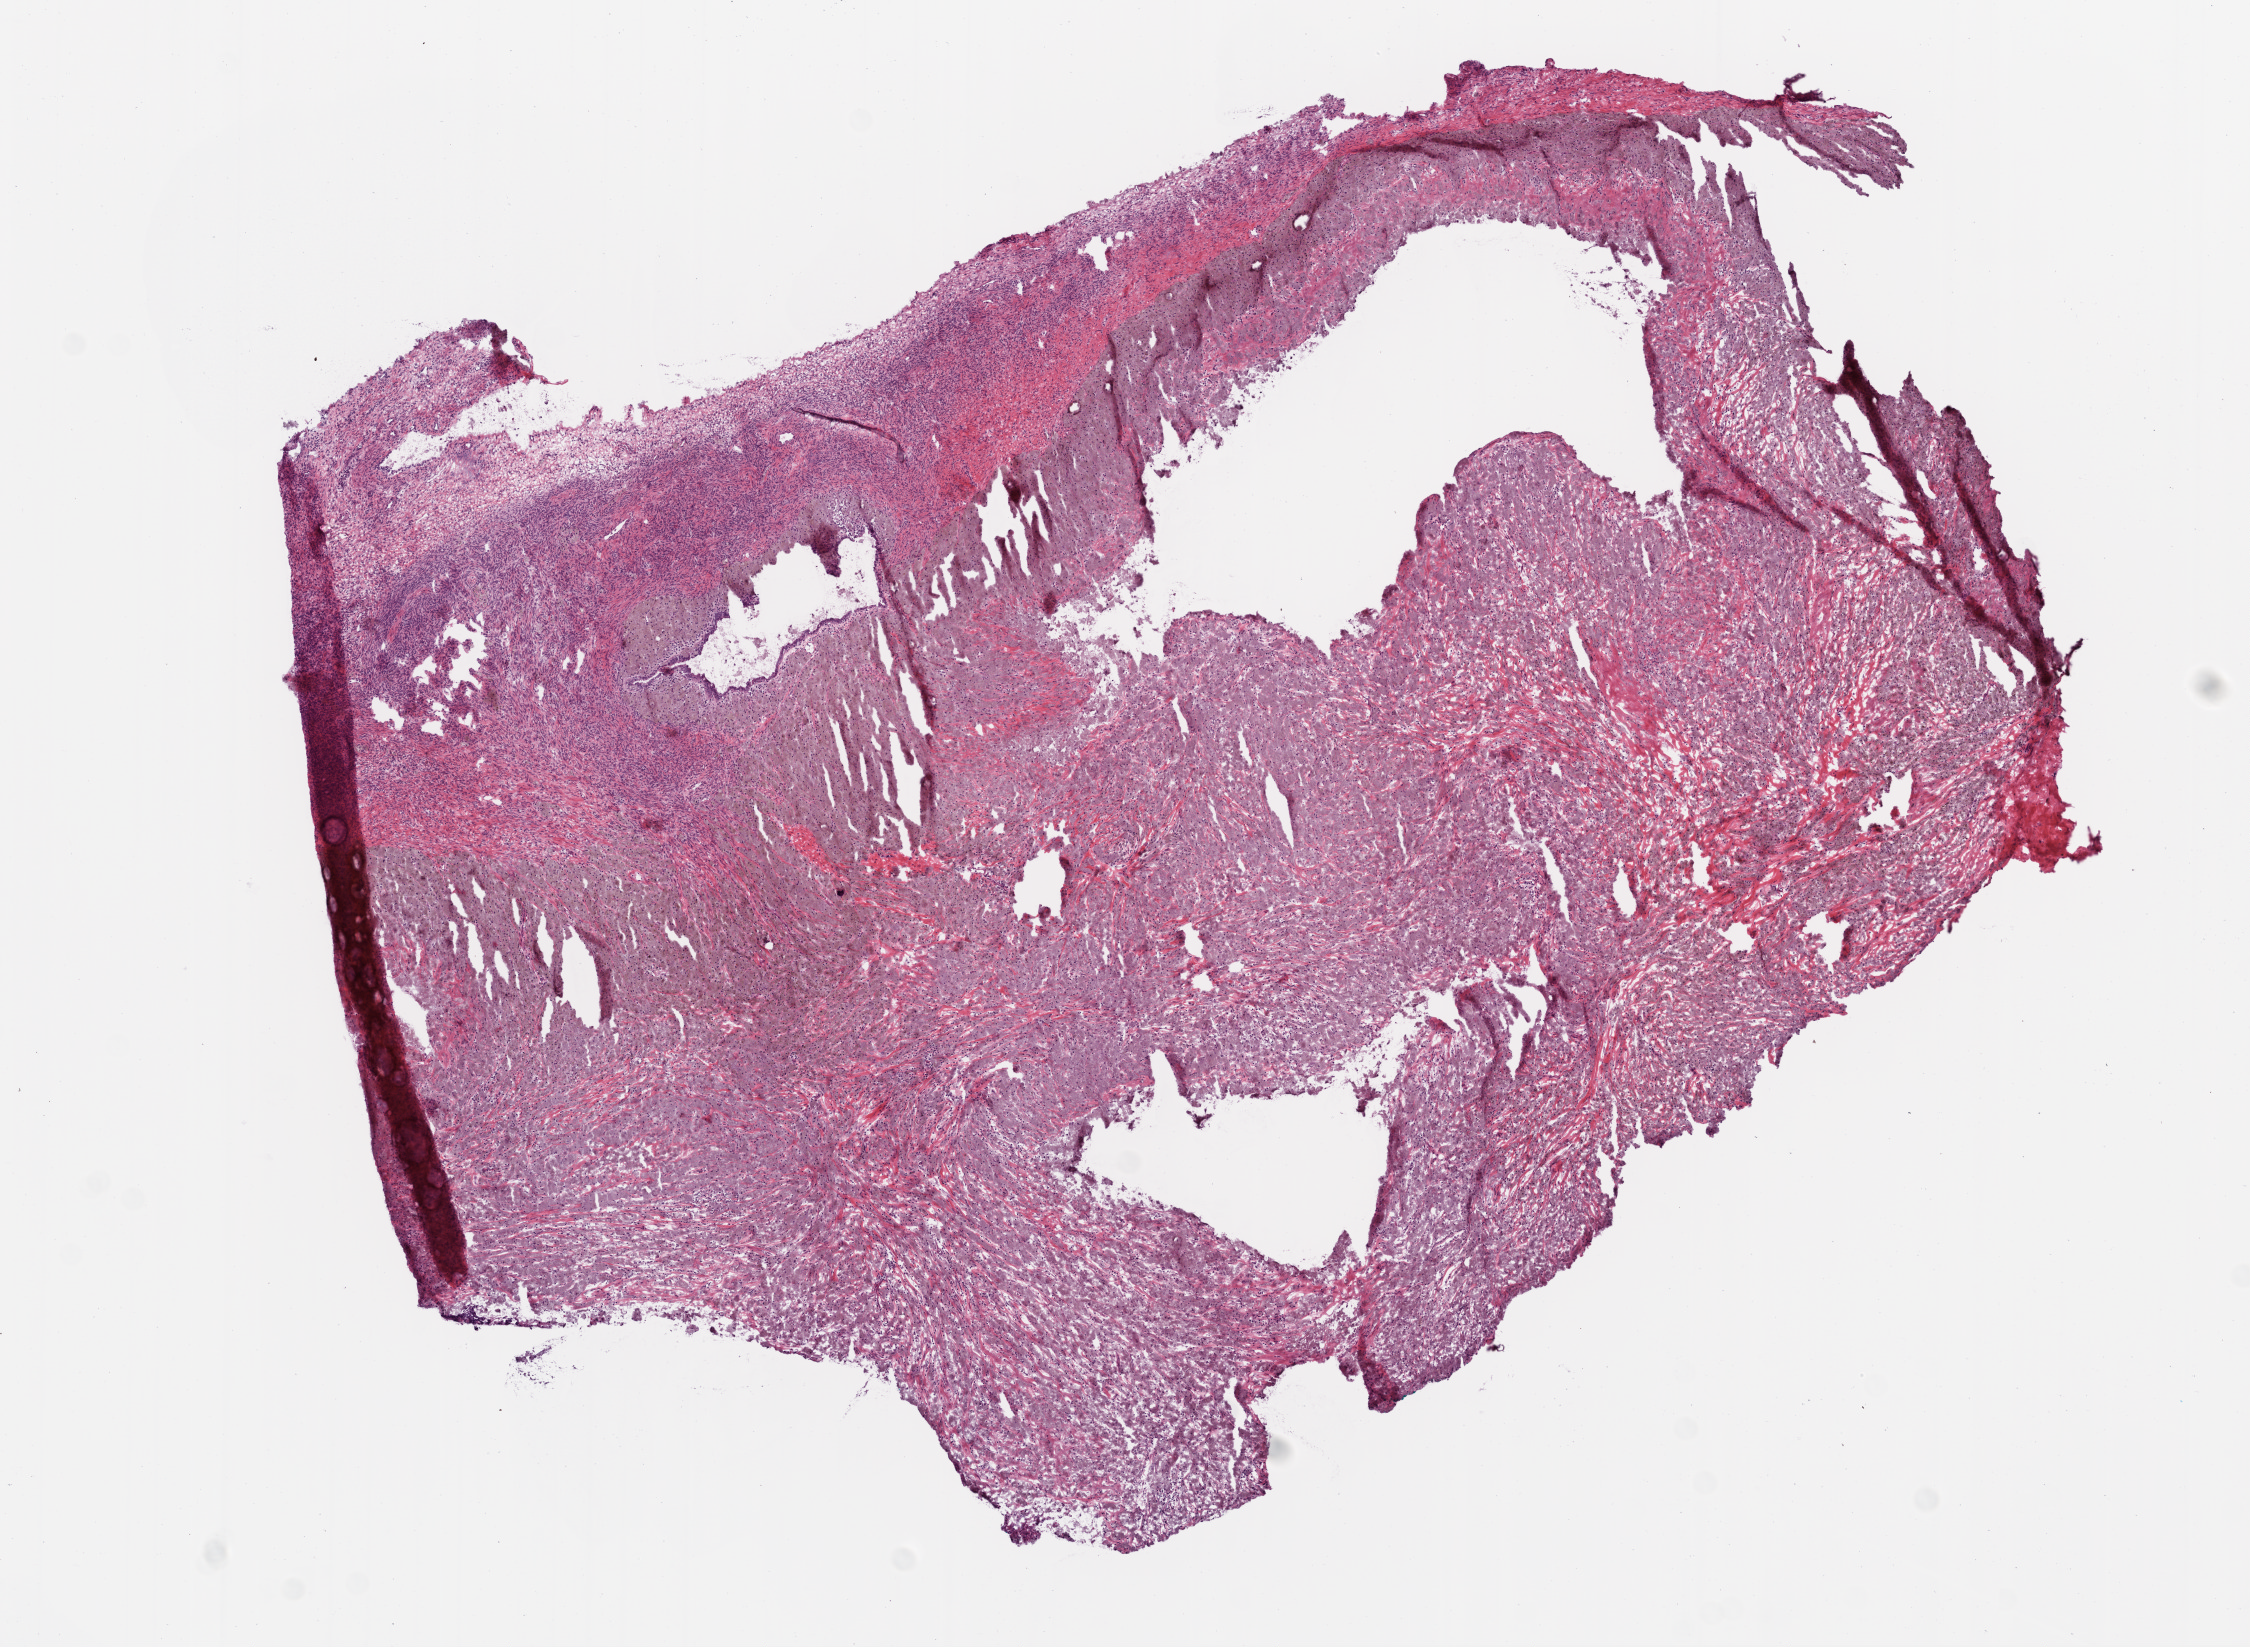
Whole-slide histology image, H&E-stained — a low-resolution overview of the entire scanned area, about 9.0 x 6.6 mm (from a 20x scan), frozen section from the top of the tissue portion, brain, primary tumour sample. Female patient; age at initial diagnosis 57 years. Histologic grade: G3 (poorly differentiated). Composition of this section per pathologist review: tumour cells 100%, tumour nuclei 75%, normal cells 0%, stromal cells 0%, necrosis 0%.
Pathologic diagnosis: Astrocytoma, anaplastic (cerebrum).